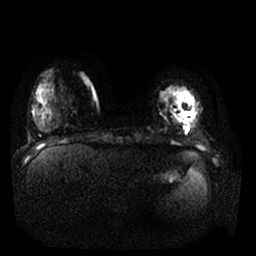
Breast MRI, one axial slice; position 2 of 25 along the scan axis; diffusion-weighted series; image 2 of 4 stored at this slice position (different b-values; order by instance number); 1.5 T; 256 × 256 image matrix. Female patient.
Outlined on this slice (expert manual segmentation):
- tumour on diffusion-weighted imaging: bounding box [x1, y1, x2, y2] px = [185, 119, 190, 122]